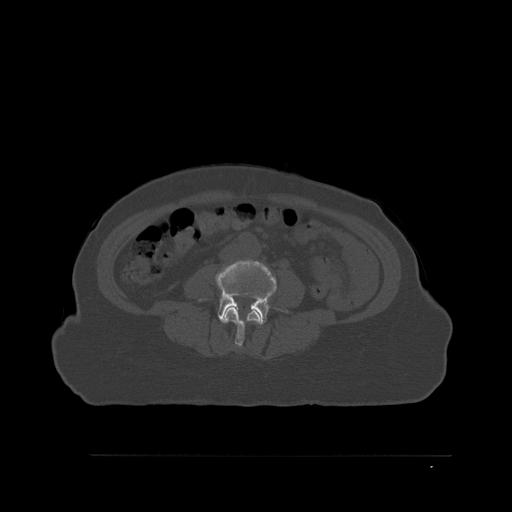
CT including the spine, one axial slice; position 214 of 527 along the scan axis; bone window (W 1800 / L 400 HU); 1.5 mm slice thickness; 512 × 512 image matrix, field of view 470 × 470 mm. Patient: female, 73 years. Case-level facts recorded for this patient, not image findings: primary cancer: breast.
Outlined on this slice (semi-automatically segmented with operator editing):
- L3 vertebra: bounding box [x1, y1, x2, y2] px = [223, 306, 261, 347]
- L4 vertebra: [200, 260, 288, 325]